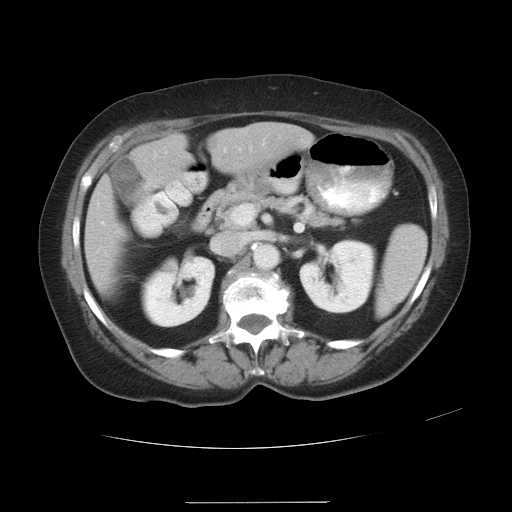
Contrast-enhanced abdominal CT, one axial slice; slice 15 of 32 in the series (ordered by position); reconstruction kernel STANDARD; intravenous contrast given; soft-tissue window (W 400 / L 40 HU); 512 × 512 image matrix, field of view 386 × 386 mm. Female patient, age 65 years. From the clinical record (not read from this slice): diagnosis: colorectal cancer liver metastases, imaged before liver resection; multiple liver metastases: yes; largest metastasis: 1.7 cm; disease in both lobes: no.
Structures marked on this image (expert manual segmentation):
- liver: bounding box <86,124,307,285> (left, top, right, bottom; pixels)
- planned liver remnant (the part of the liver to remain after resection): <86,137,186,285>